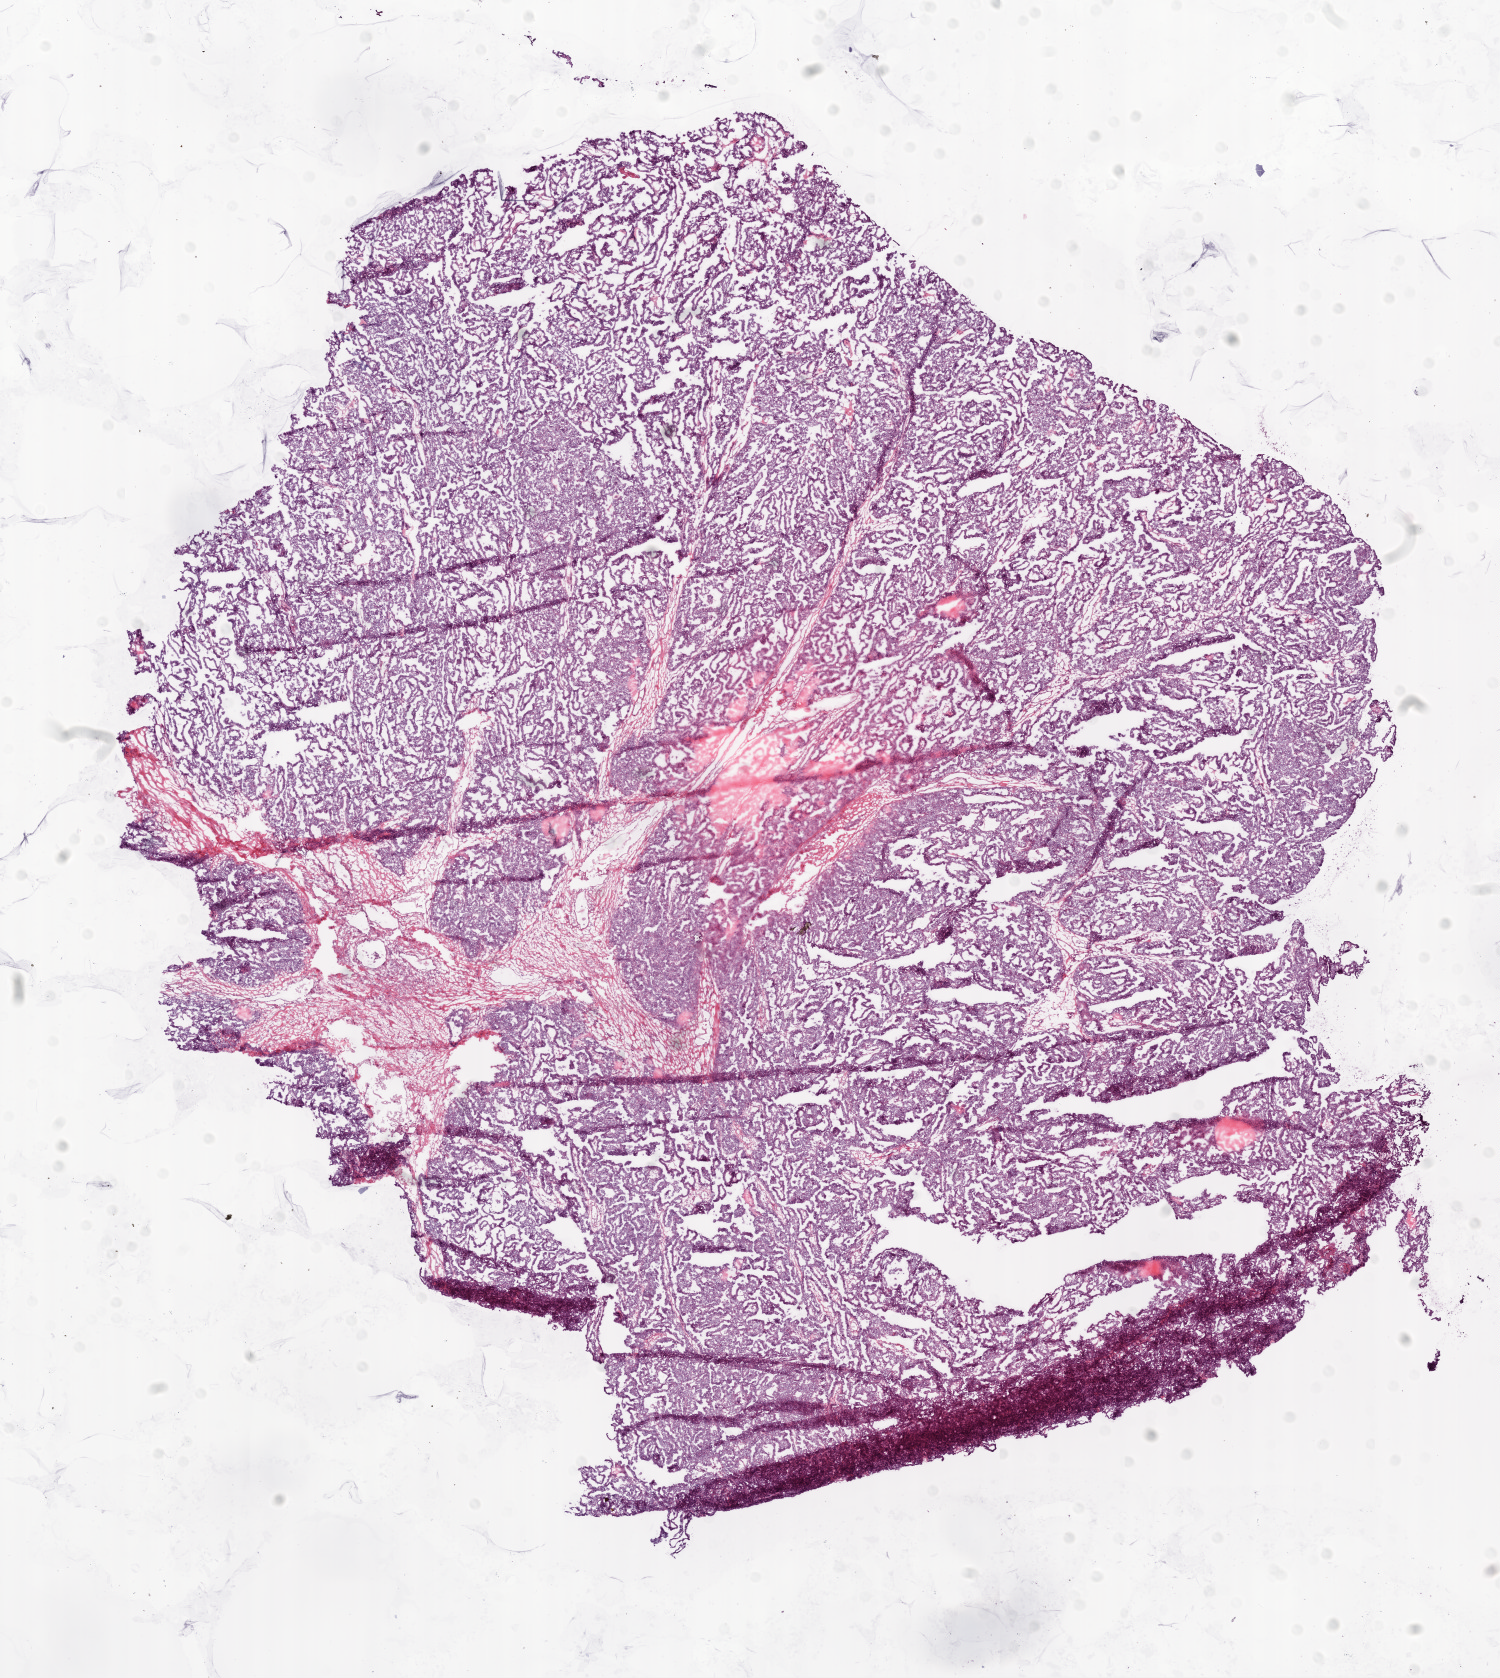
Whole-slide histology image, H&E-stained — shown as a low-resolution overview of the whole scanned area (about 12.0 x 13.5 mm); frozen section from the bottom of the tissue portion; sample: primary tumour, ovary. Female patient; age at initial diagnosis 51 years. Histologic grade: G3 (poorly differentiated). Pathologist review of this section (percent, as recorded): tumour cells 94%, tumour nuclei 95%, normal cells 0%, stromal cells 5%, necrosis 1%.
FIGO stage: IIIC. Laterality: bilateral. Histologic diagnosis: Serous cystadenocarcinoma, NOS.